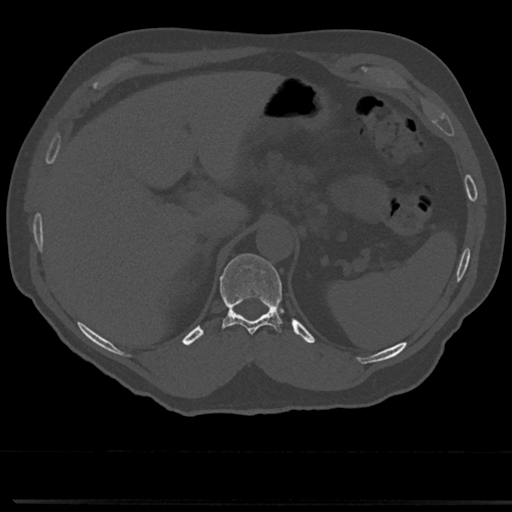
CT including the spine, one axial slice; reconstruction kernel Br40s/3; 120 kVp; bone window (W 1800 / L 400 HU); 512 × 512 image matrix, field of view 355 × 355 mm. Patient: male, 61 years. Case-level facts recorded for this patient, not image findings: primary cancer: prostate.
Structures marked on this image (semi-automatically segmented with operator editing):
- T11 vertebra: bounding box <220,254,283,335> (left, top, right, bottom; pixels)